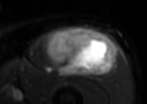
MRI of an extremity soft-tissue mass, one axial slice; position 49 of 85 along the scan axis; T2-weighted fat-saturated; MR volume resampled by the dataset authors to the PET/CT grid (not the native acquisition matrix); 3.27 mm slice thickness; 147 × 104 image matrix, field of view 144 × 102 mm. Male patient. Case-level facts recorded for this patient, not image findings: histological type: extraskeletal osteosarcoma; grade: high; site of the primary tumour: thigh.
Structures marked on this image (expert contour drawn on MRI and transferred to this co-registered scan by the dataset authors):
- gross tumour volume (mass): bounding box <46,28,116,77> (left, top, right, bottom; pixels)